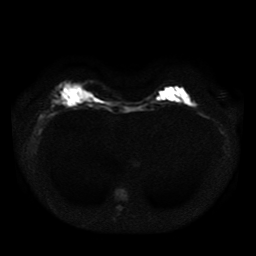
Breast MRI, one axial slice. Position 12 of 41 along the scan axis. Diffusion-weighted series; image 2 of 4 stored at this slice position (different b-values; order by instance number). 1.5 T. 5 mm slice thickness. 256 × 256 image matrix, field of view 330 × 330 mm. Female patient.
Annotated regions visible in this slice (manually delineated by an expert):
- tumour on diffusion-weighted imaging: box from (x=54, y=98) to (x=60, y=105) px